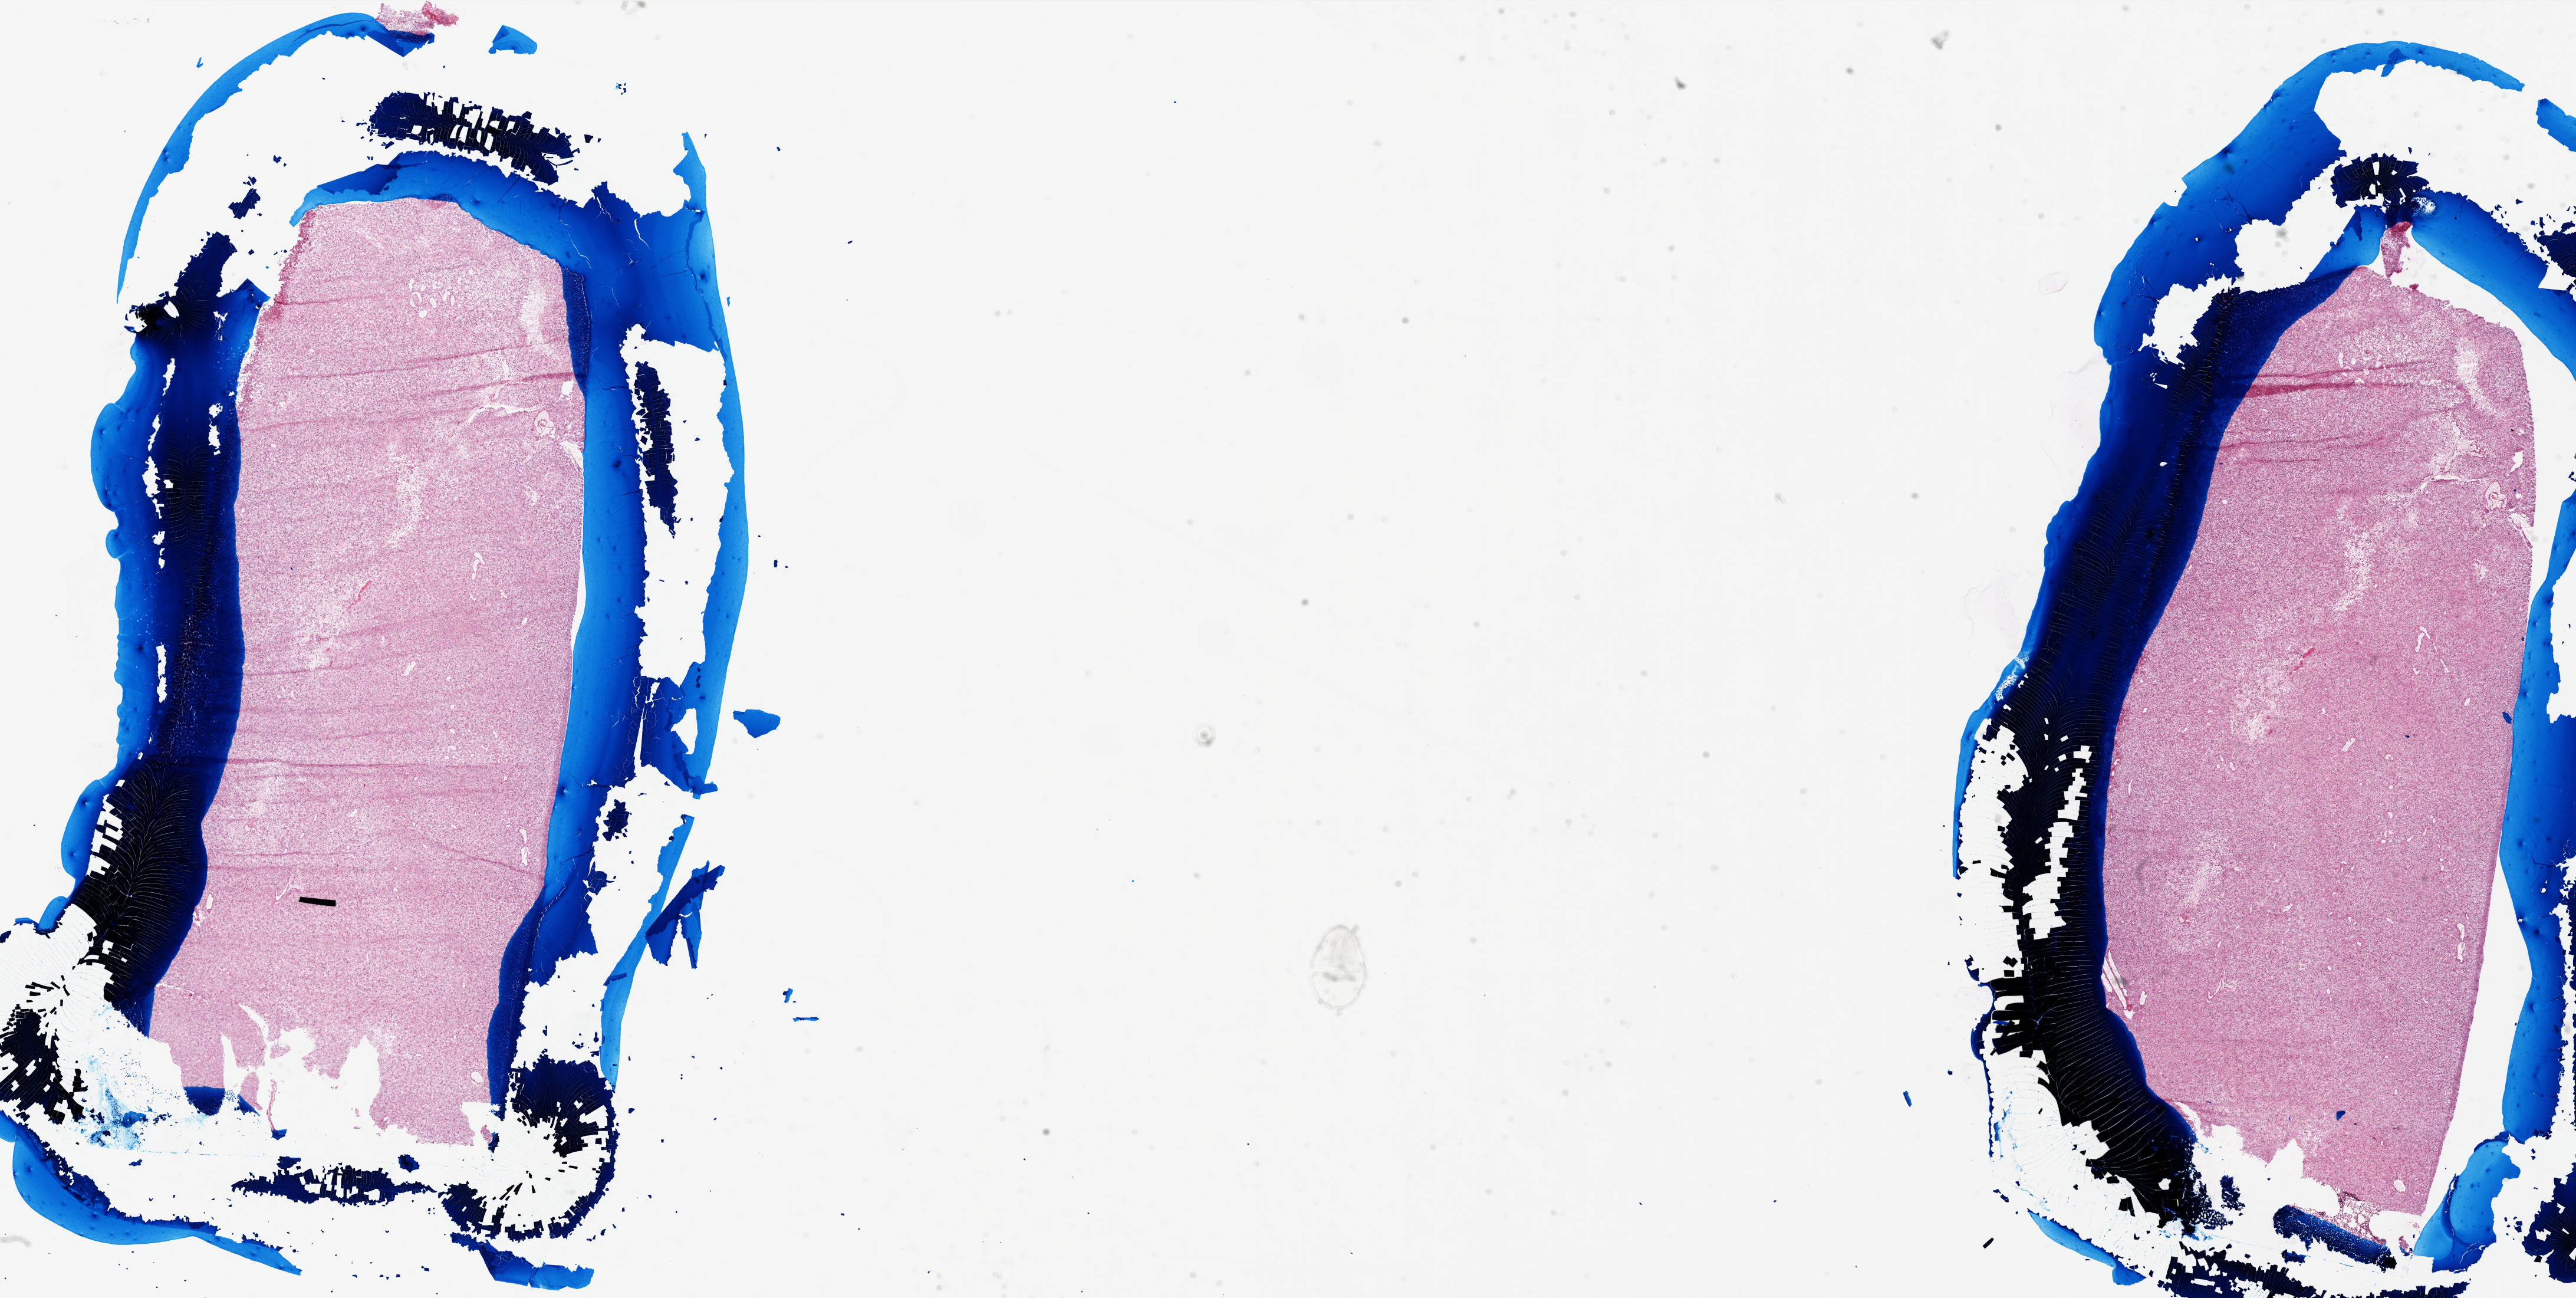
Digitized H&E tissue section (whole slide) — low-resolution overview of the scanned area, about 35.0 x 17.6 mm; frozen section from the top of the tissue portion; primary tumour sample from the brain. Male patient; age at initial diagnosis 61 years. Slide review estimates, as recorded: tumour cells 90%, tumour nuclei 100%, normal cells 0%, stromal cells 0%, necrosis 10%.
• diagnosis: Glioblastoma